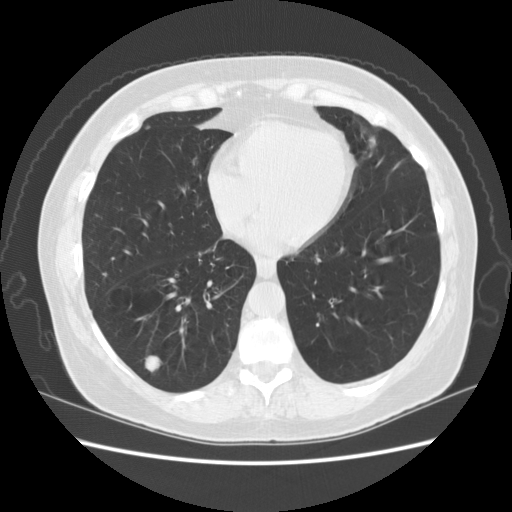
Axial slice from a low-dose chest CT screening exam. Third screening round (two years after baseline). Lung window (W 1500 / L -600 HU). 2.5 mm slice thickness. Female, age 59 years at enrolment. Current smoker at enrolment.
- Expert-annotated lung lesion, bounding box <134,347,171,384> (left, top, right, bottom; pixels).
- Screening reader's record for this exam (one nodule recorded; not confirmed to be the boxed lesion): non-calcified nodule or mass ≥4 mm, right lower lobe, 16 × 11 mm, smooth margins, soft tissue attenuation, pre-existing on the prior screen: yes; interval growth: yes.
- Lung cancer was diagnosed 42 days after this screen: non-small cell carcinoma, right lower lobe, poorly differentiated (G3), stage IA (AJCC 6th edition), 15 mm at pathology.